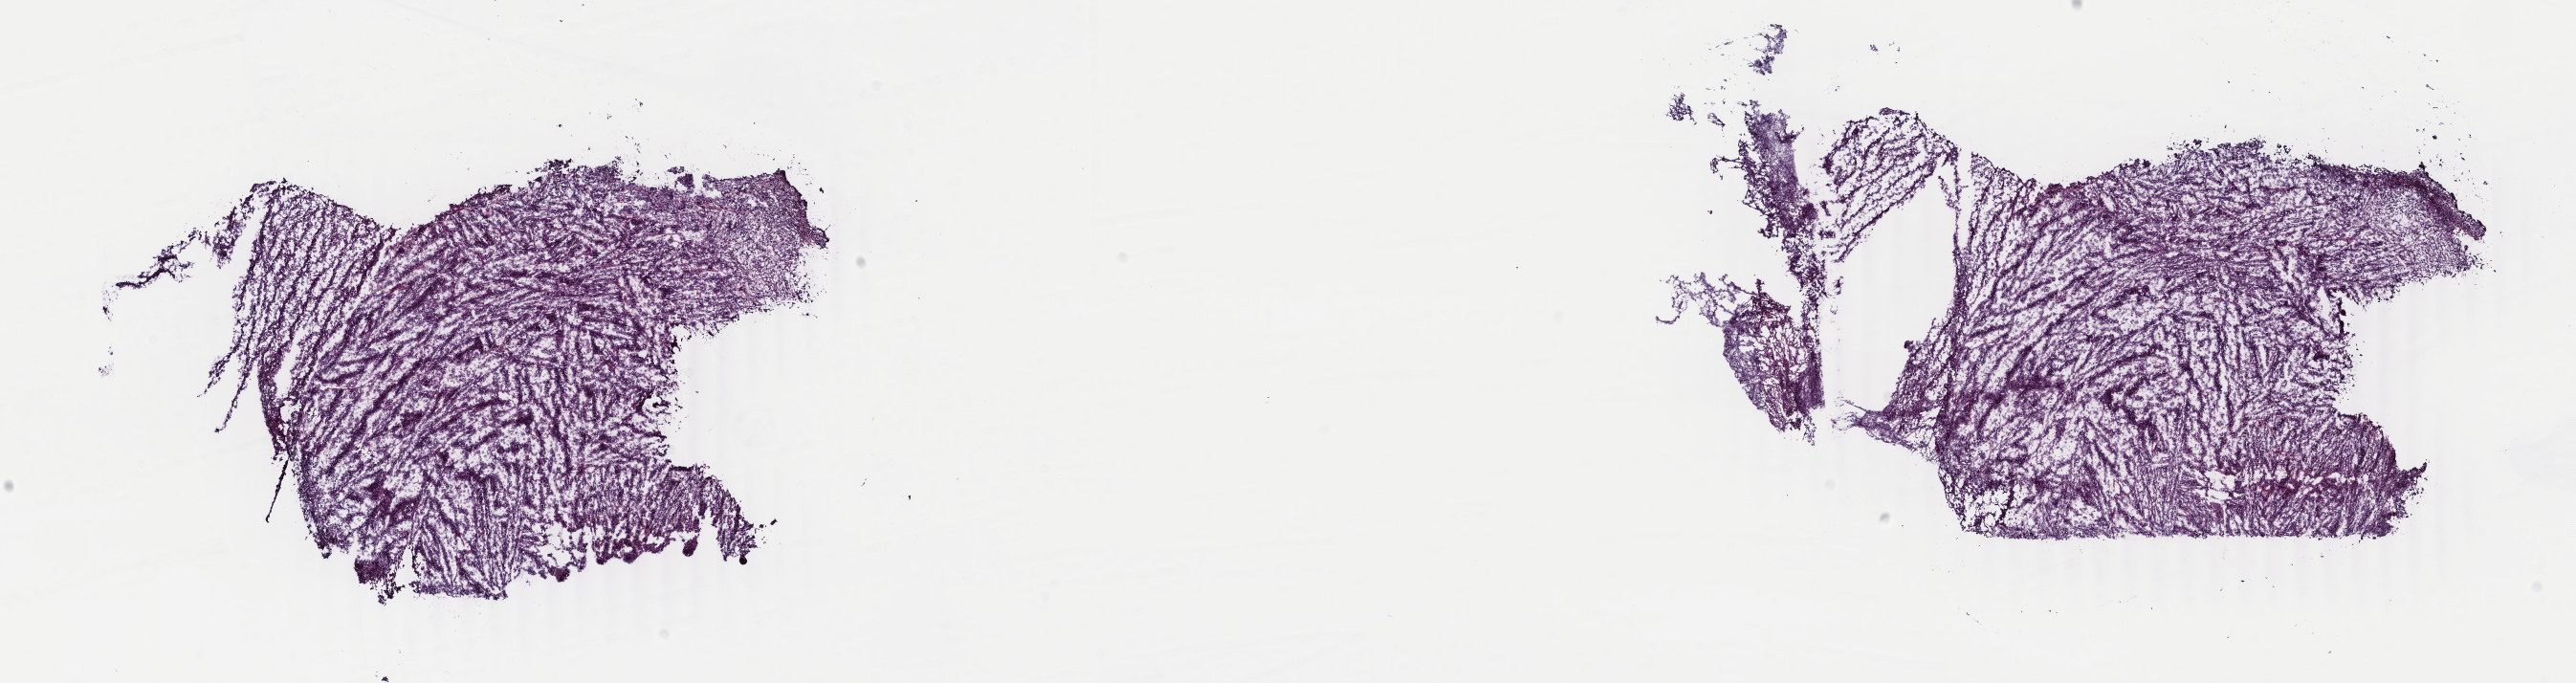
Whole-slide histology image, H&E-stained — whole scanned area (about 21.4 x 5.7 mm, from a 40x scan) shown as a low-resolution overview, frozen section from the top of the tissue portion, sample: primary tumour, uterus. Female, age 62 years at initial diagnosis. Slide review estimates, as recorded: tumour cells 85%, tumour nuclei 90%, normal cells 0%, stromal cells 0%, necrosis 15%. Infiltration values recorded for this section: lymphocyte infiltration 0%, monocyte infiltration 0%, neutrophil infiltration 0%.
FIGO stage: IVB. Diagnosis: Mullerian mixed tumor (endometrium).